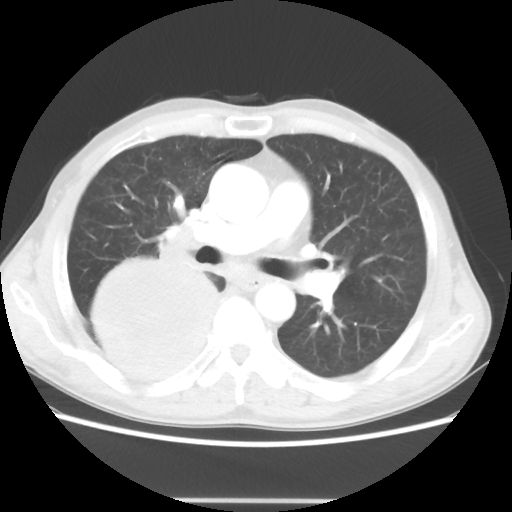
Chest CT, one axial slice. Position 28 of 48 along the scan axis. Lung window (W 1500 / L -600 HU). 5 mm slice thickness. 512 × 512 image matrix, field of view 361 × 361 mm. Male patient, age 66 years. Case-level facts recorded for this patient, not image findings: clinical TNM (as recorded): T4 N1 M1.
Structures marked on this image (rectangle marked by the reading radiologist):
- lung tumour (recorded histology: small cell carcinoma): box from (x=78, y=250) to (x=225, y=393) px